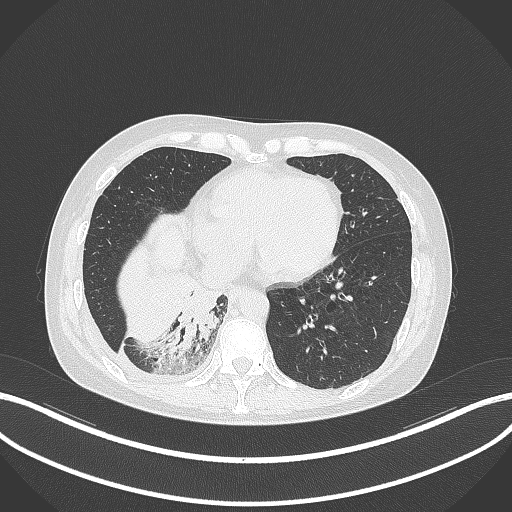
Chest CT, one axial slice; position 93 of 329 along the scan axis; reconstruction kernel B70f; 120 kVp; lung window (W 1500 / L -600 HU); 1 mm slice thickness; 512 × 512 image matrix, field of view 400 × 400 mm. Patient: female, 63 years. Case-level facts recorded for this patient, not image findings: clinical TNM (as recorded): T1c N0 M0.
Structures marked on this image (rectangle marked by the reading radiologist):
- lung tumour (recorded histology: adenocarcinoma): bounding box (x1, y1, x2, y2) in pixels: (166, 281, 219, 361)